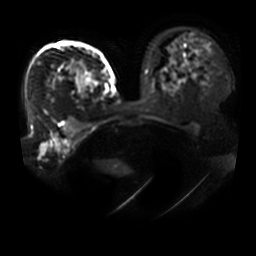
Breast MRI, one axial slice; slice 29 of 41 in the series (ordered by position); diffusion-weighted series; image 2 of 4 stored at this slice position (different b-values; order by instance number); 3 T; 5 mm slice thickness; 256 × 256 image matrix. Female patient.
Outlined on this slice (manually delineated by an expert):
- tumour on diffusion-weighted imaging: bounding box (x1, y1, x2, y2) in pixels: (68, 62, 97, 93)